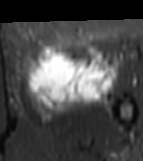
MRI of an extremity soft-tissue mass, one axial slice; slice 32 of 81 in the series (ordered by position); STIR; MR volume resampled by the dataset authors to the PET/CT grid (not the native acquisition matrix); 143 × 161 image matrix, field of view 140 × 157 mm. Female patient. From the clinical record (not read from this slice): histological type: myxofibrosarcoma; grade: intermediate; site of the primary tumour: left thigh.
Structures marked on this image (expert contour drawn on MRI and transferred to this co-registered scan by the dataset authors):
- gross tumour volume including surrounding oedema: box from (x=26, y=44) to (x=118, y=120) px
- gross tumour volume (mass): (x=26, y=44)–(x=114, y=105)